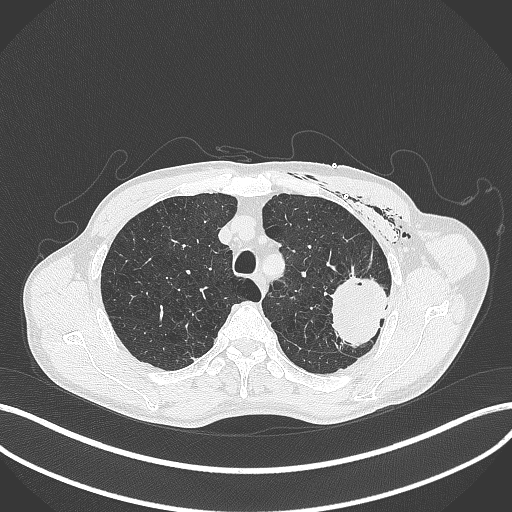
Chest CT, one axial slice; position 319 of 457 along the scan axis; reconstruction kernel B70f; 120 kVp; lung window (W 1500 / L -600 HU); 1 mm slice thickness; 512 × 512 image matrix, field of view 400 × 400 mm. Patient: male, 58 years. From the clinical record (not read from this slice): clinical TNM (as recorded): T3 N0 M0.
Structures marked on this image (rectangle marked by the reading radiologist):
- lung tumour (recorded histology: adenocarcinoma): bounding box <327,270,387,354> (left, top, right, bottom; pixels)